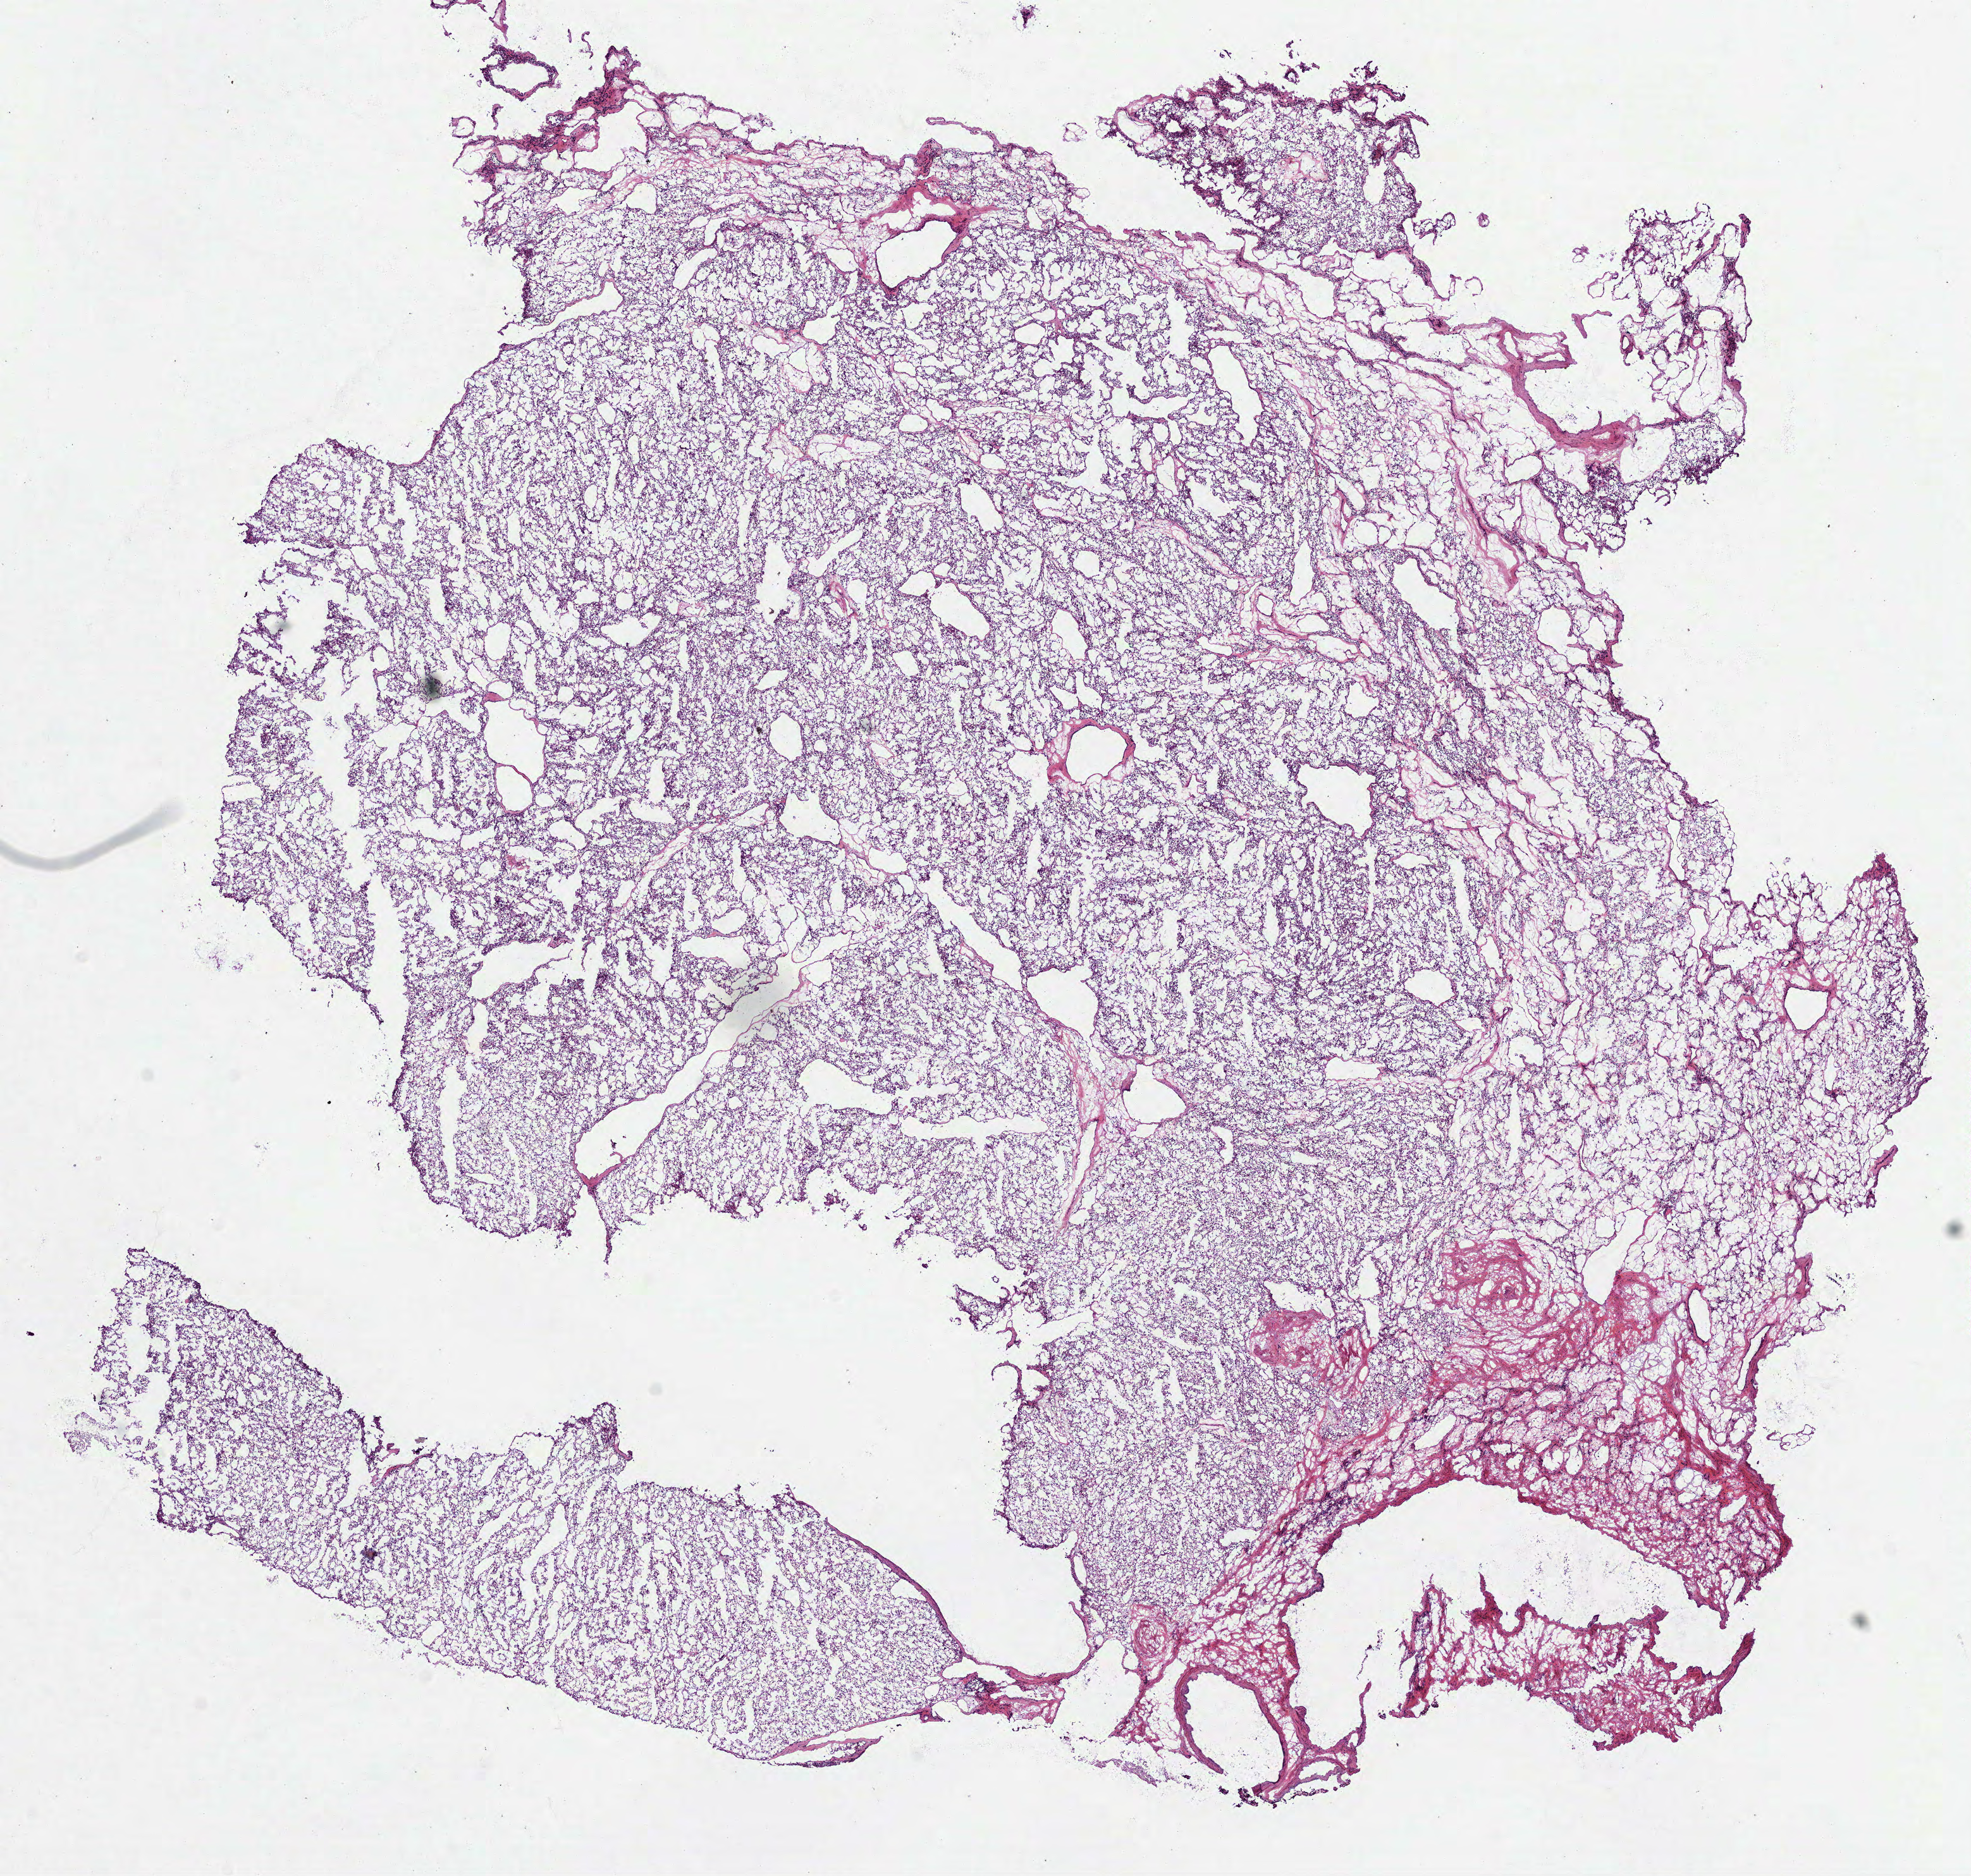
Whole-slide histology image, H&E — low-resolution overview of the scanned area, about 12.6 x 12.0 mm; frozen section; kidney, primary tumour sample. Female, age 59 years at initial diagnosis. Histologic grade: G2 (moderately differentiated). Slide review estimates, as recorded: tumour cells 90%, tumour nuclei 85%, normal cells 0%, stromal cells 10%, necrosis 0%.
AJCC pathologic stage: I. Pathologic diagnosis: Clear cell adenocarcinoma, NOS.